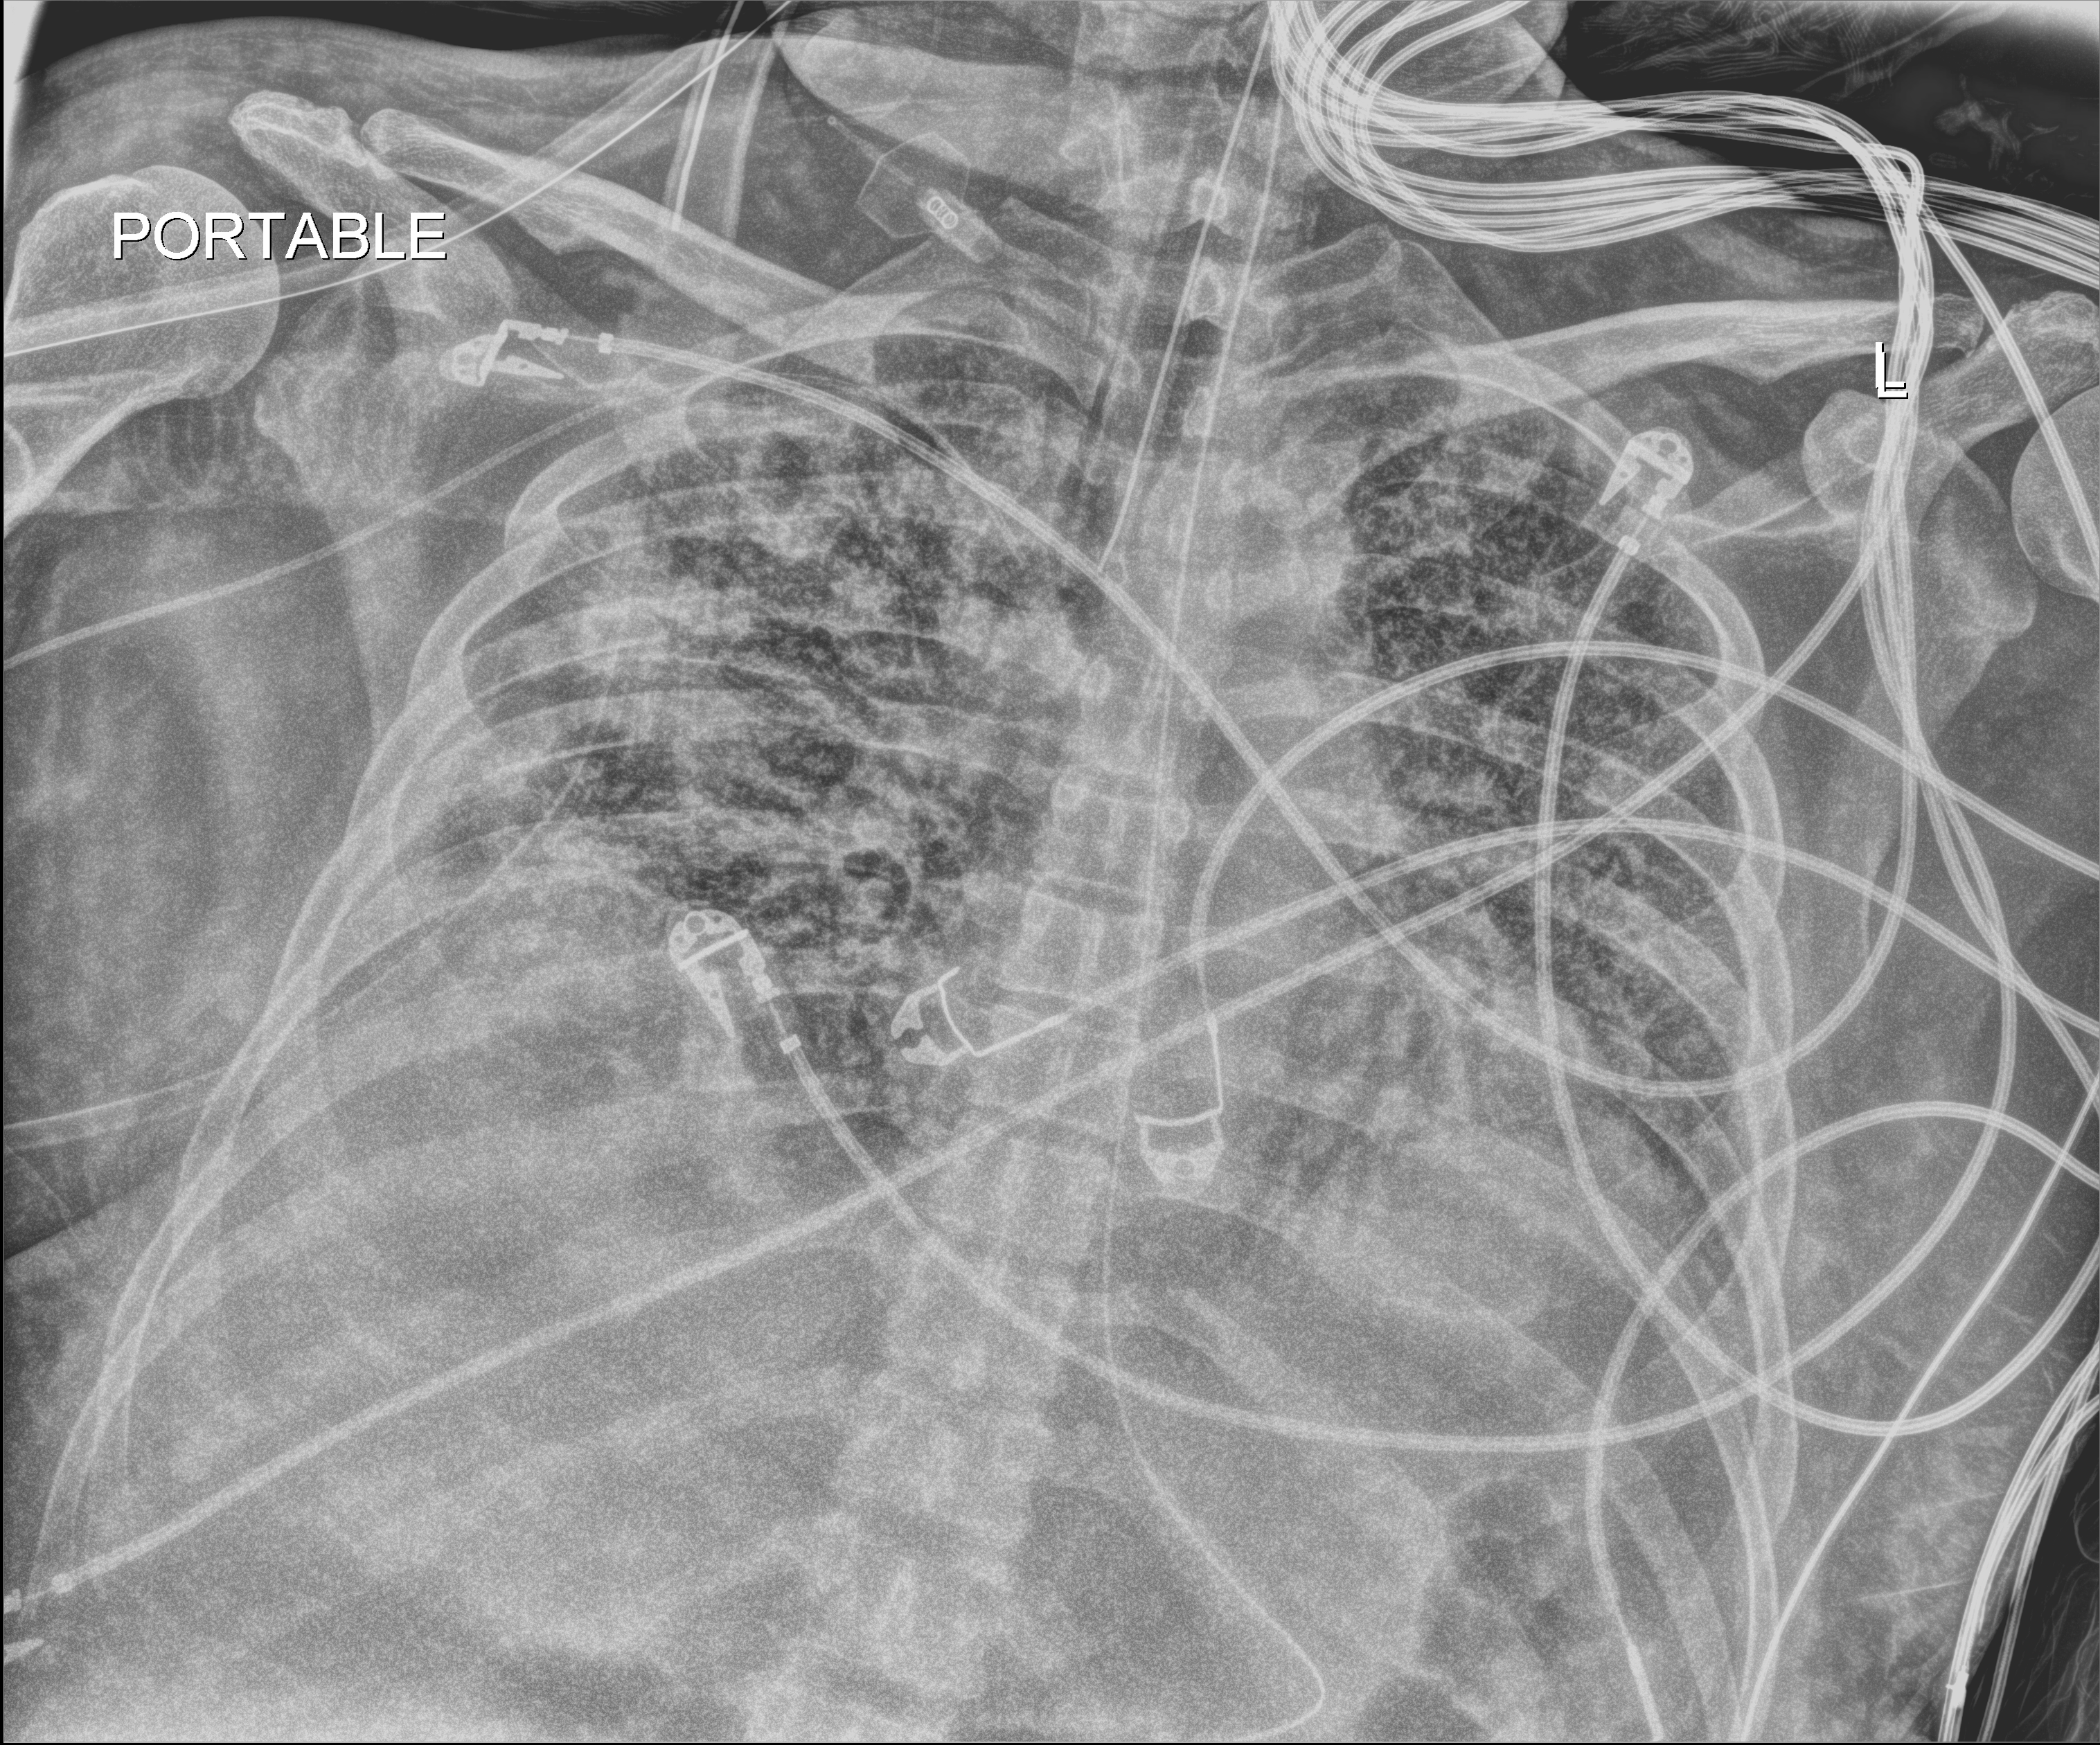
Bedside chest radiograph (digital radiography); anteroposterior (AP) projection. Male patient hospitalised with COVID-19, age 18–59 years.
Admission-level facts for this patient (not findings on this image; timing relative to this image not recorded): length of hospital stay: 96 days; mechanically ventilated during this hospital stay: yes.